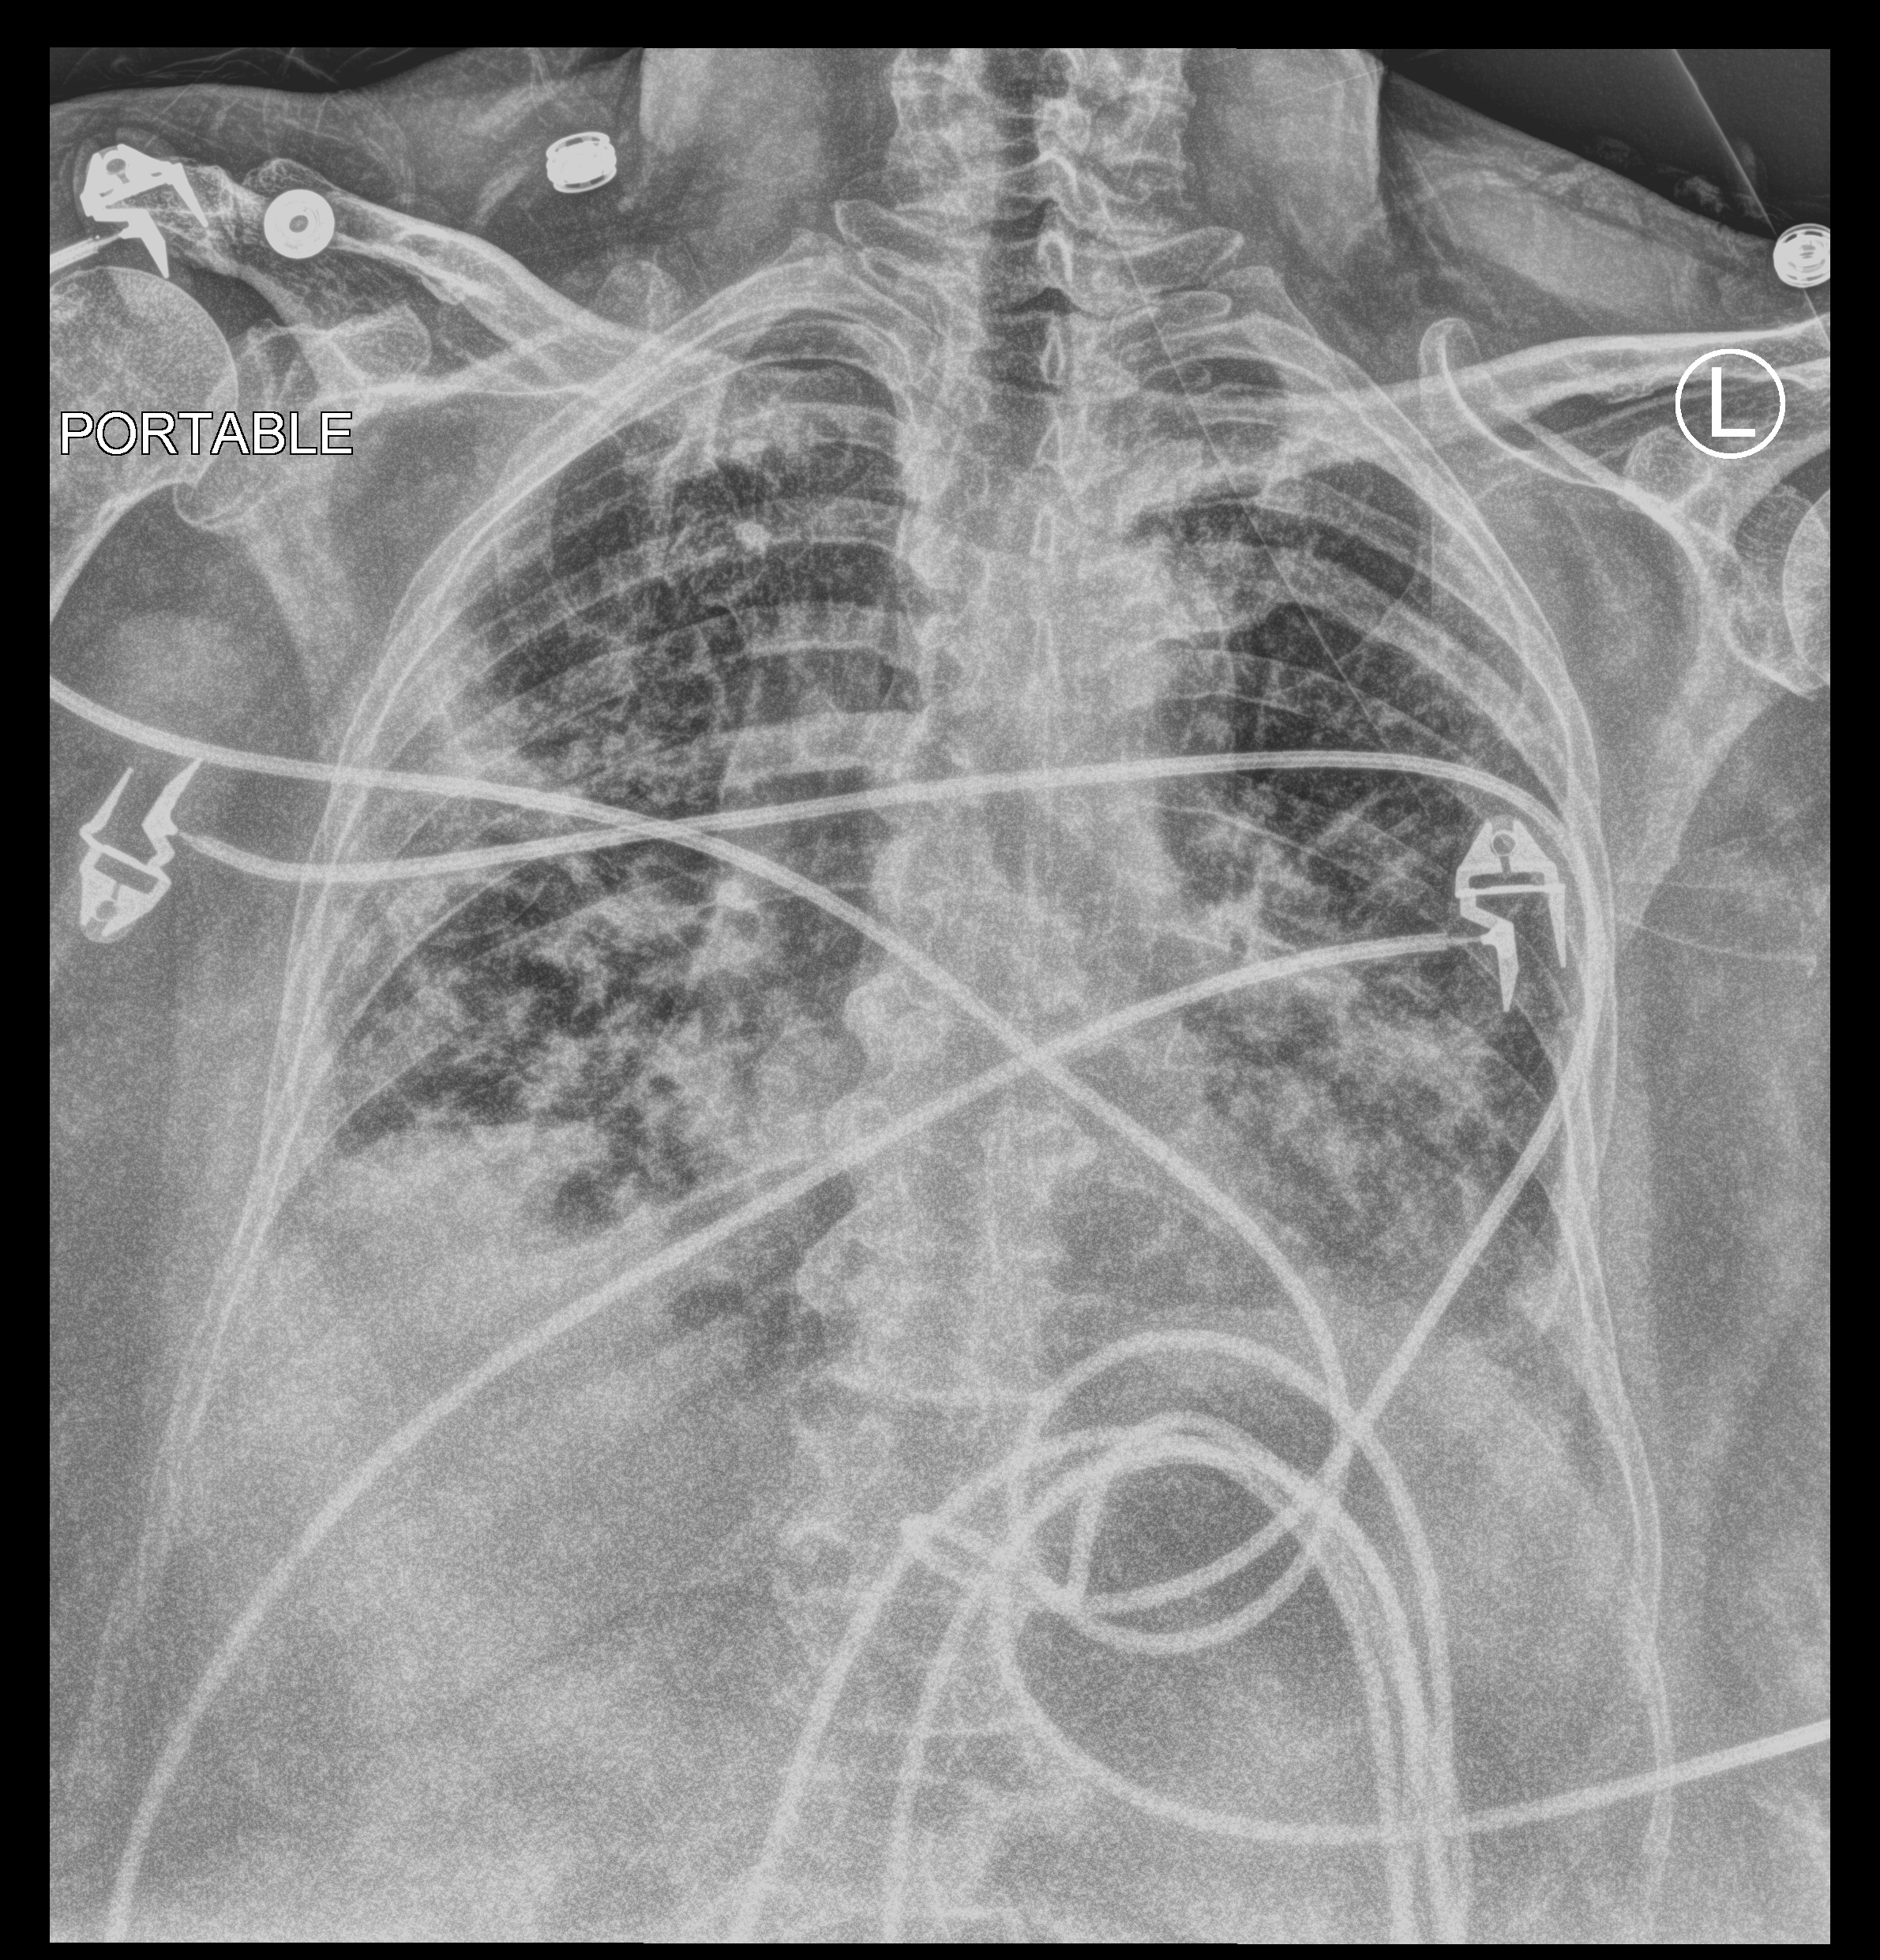
Portable chest radiograph; anteroposterior (AP) projection. Patient hospitalised with COVID-19; female, aged 75–90 years.
Admission-level facts for this patient (not findings on this image; timing relative to this image not recorded): admitted to intensive care during this hospital stay: yes.